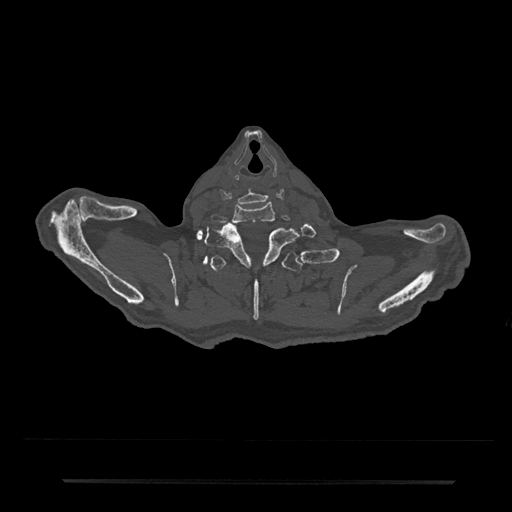
CT including the spine, one axial slice; position 719 of 797 along the scan axis; 120 kVp; bone window (W 1800 / L 400 HU); 0.5 mm slice thickness; 512 × 512 image matrix, field of view 427 × 427 mm. Male patient, age 74 years. From the clinical record (not read from this slice): primary cancer: prostate.
Structures marked on this image (semi-automatically segmented with operator editing):
- T1 vertebra: box from (x=204, y=223) to (x=299, y=267) px
- T2 vertebra: (x=202, y=251)–(x=314, y=320)